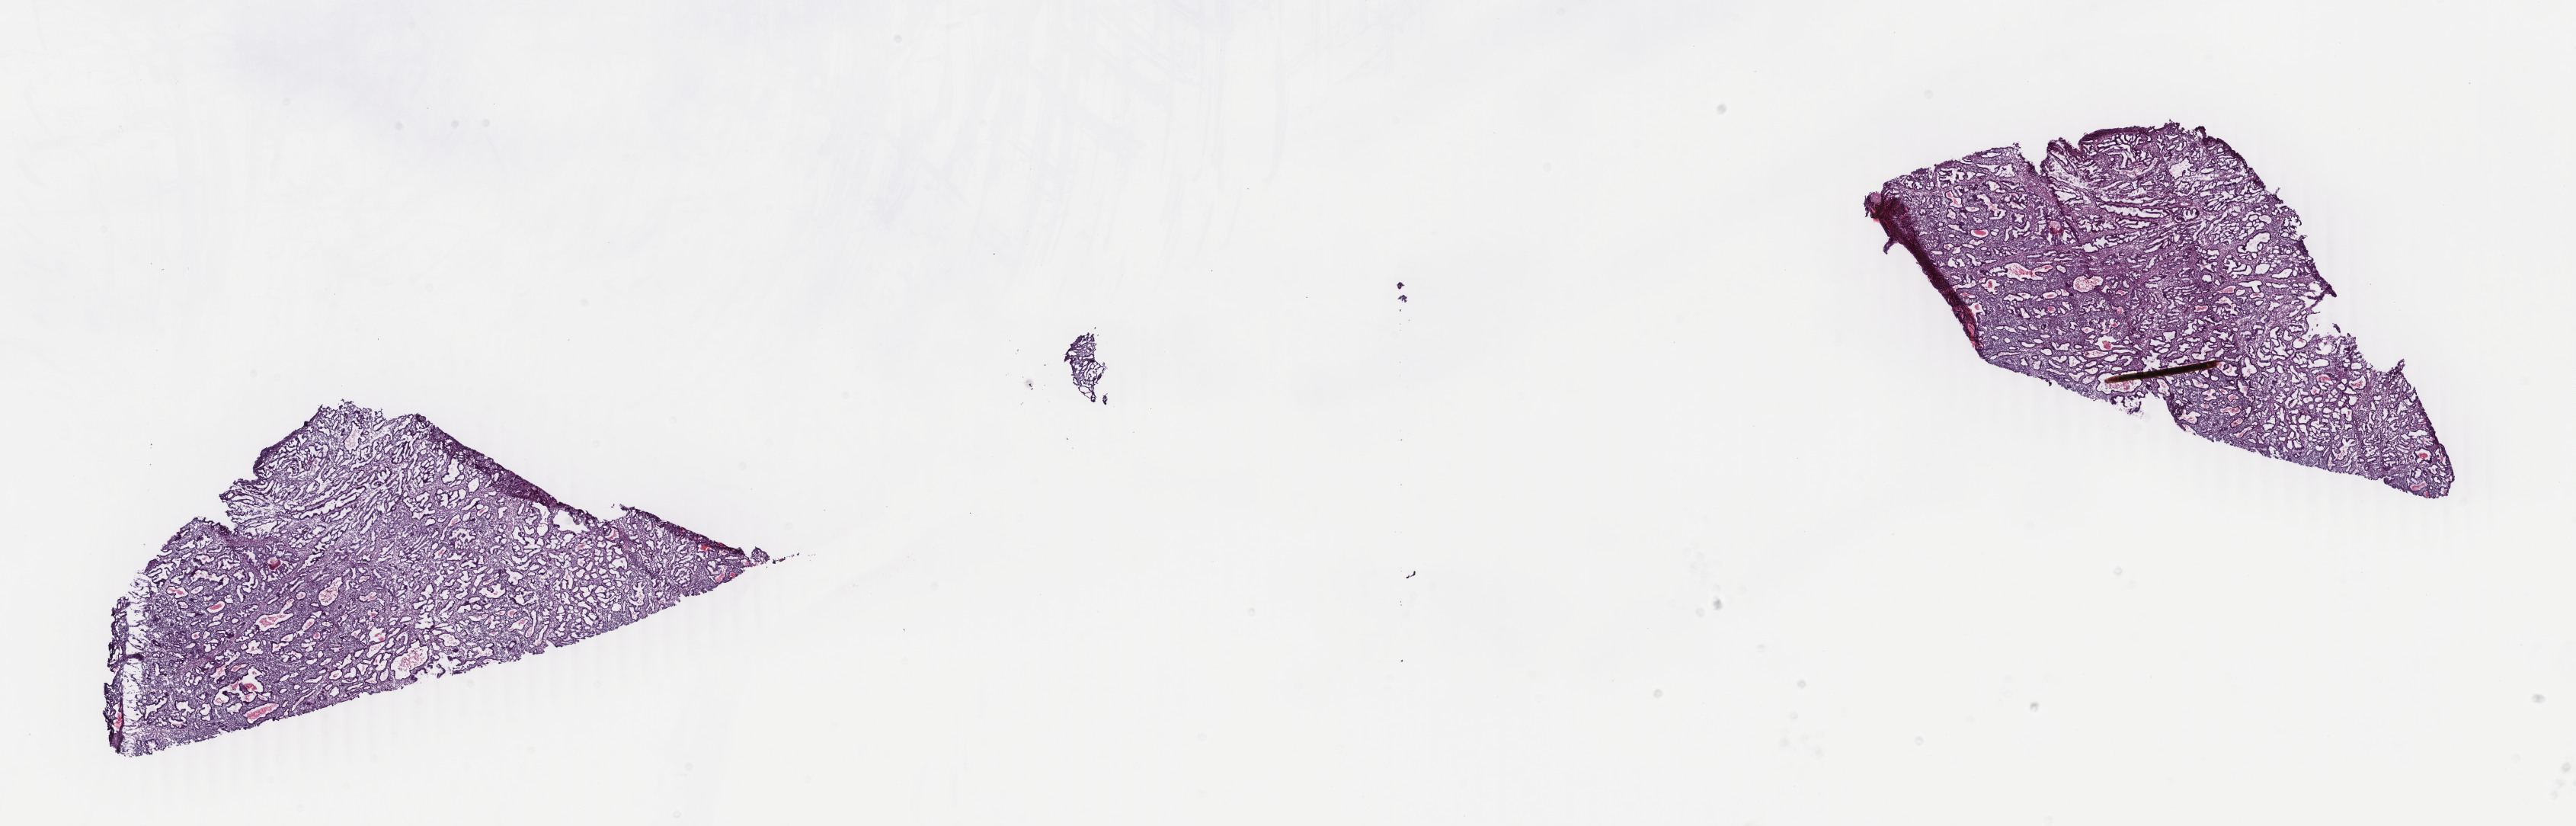
Whole-slide histology image, H&E — a low-resolution overview of the entire scanned area, about 26.9 x 8.6 mm (acquisition: 40x scan); frozen section from the top of the tissue portion; sample: primary tumour, uterus. Patient: female, age at initial diagnosis 51 years. Histologic grade: G3 (poorly differentiated). Composition of this section per pathologist review: tumour cells 40%, tumour nuclei 60%, normal cells 30%, stromal cells 30%, necrosis 0%. Infiltration values recorded for this section: lymphocyte infiltration 40%, monocyte infiltration 10%, neutrophil infiltration 20%.
Lymph nodes positive (case pathology): 0 of 9 examined. Histologic diagnosis: Endometrioid adenocarcinoma, NOS (endometrium). FIGO stage: IA.